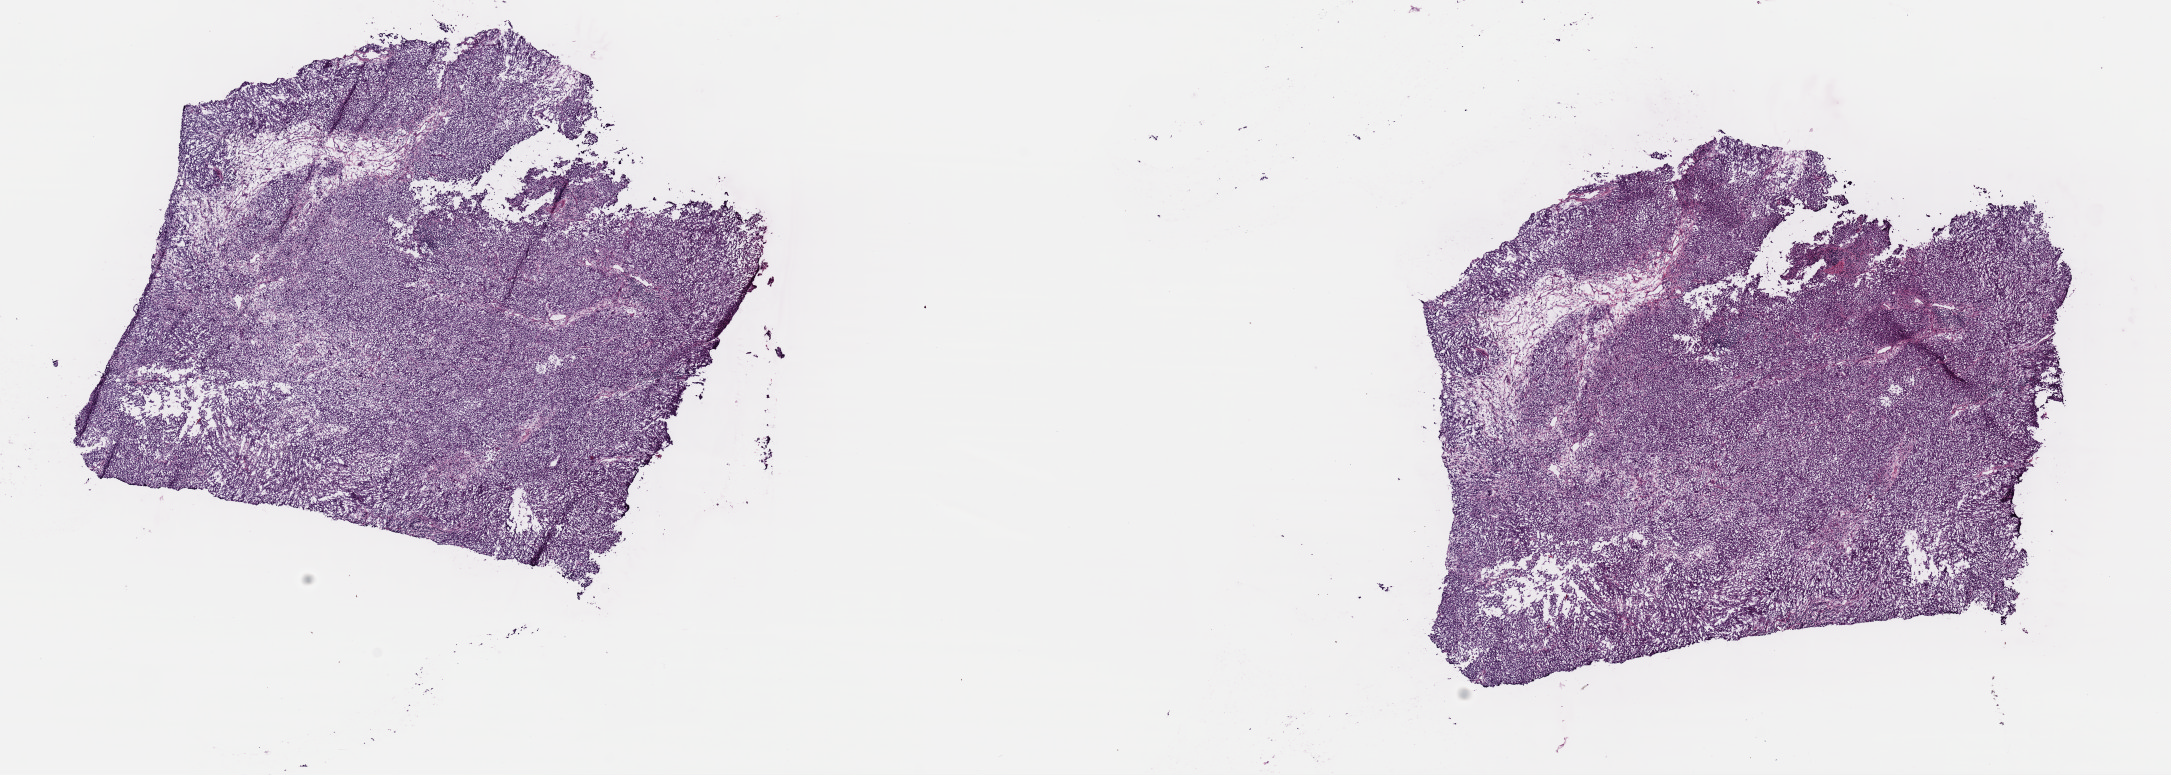
Digitized H&E tissue section (whole slide) — low-resolution overview of the scanned area, about 17.2 x 6.1 mm, frozen section from the top of the tissue portion, metastatic tumour sample, sampled site not recorded. Patient sex: male. Pathologist review of this section (percent, as recorded): tumour cells 100%, tumour nuclei 95%, normal cells 0%, stromal cells 0%, necrosis 0%. Infiltration values recorded for this section: lymphocyte infiltration 0%, monocyte infiltration 0%, neutrophil infiltration 0%.
* this section: metastatic tumour tissue
* patient diagnosis: Malignant melanoma, NOS